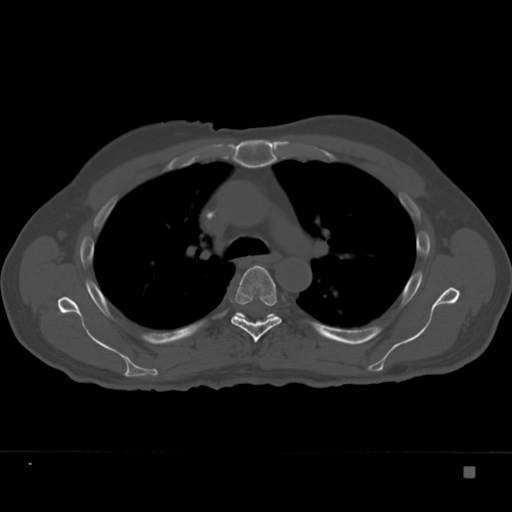
CT including the spine, one axial slice; slice 255 of 332 in the series (ordered by position); reconstruction kernel Br40s; 120 kVp; bone window (W 1800 / L 400 HU); 1.5 mm slice thickness; 512 × 512 image matrix. Patient: male, 72 years. From the clinical record (not read from this slice): primary cancer: skeletal.
Outlined on this slice (semi-automatic segmentation, software-assisted and operator-edited):
- T5 vertebra: box from (x=230, y=265) to (x=282, y=343) px
- T6 vertebra: (x=235, y=312)–(x=276, y=320)